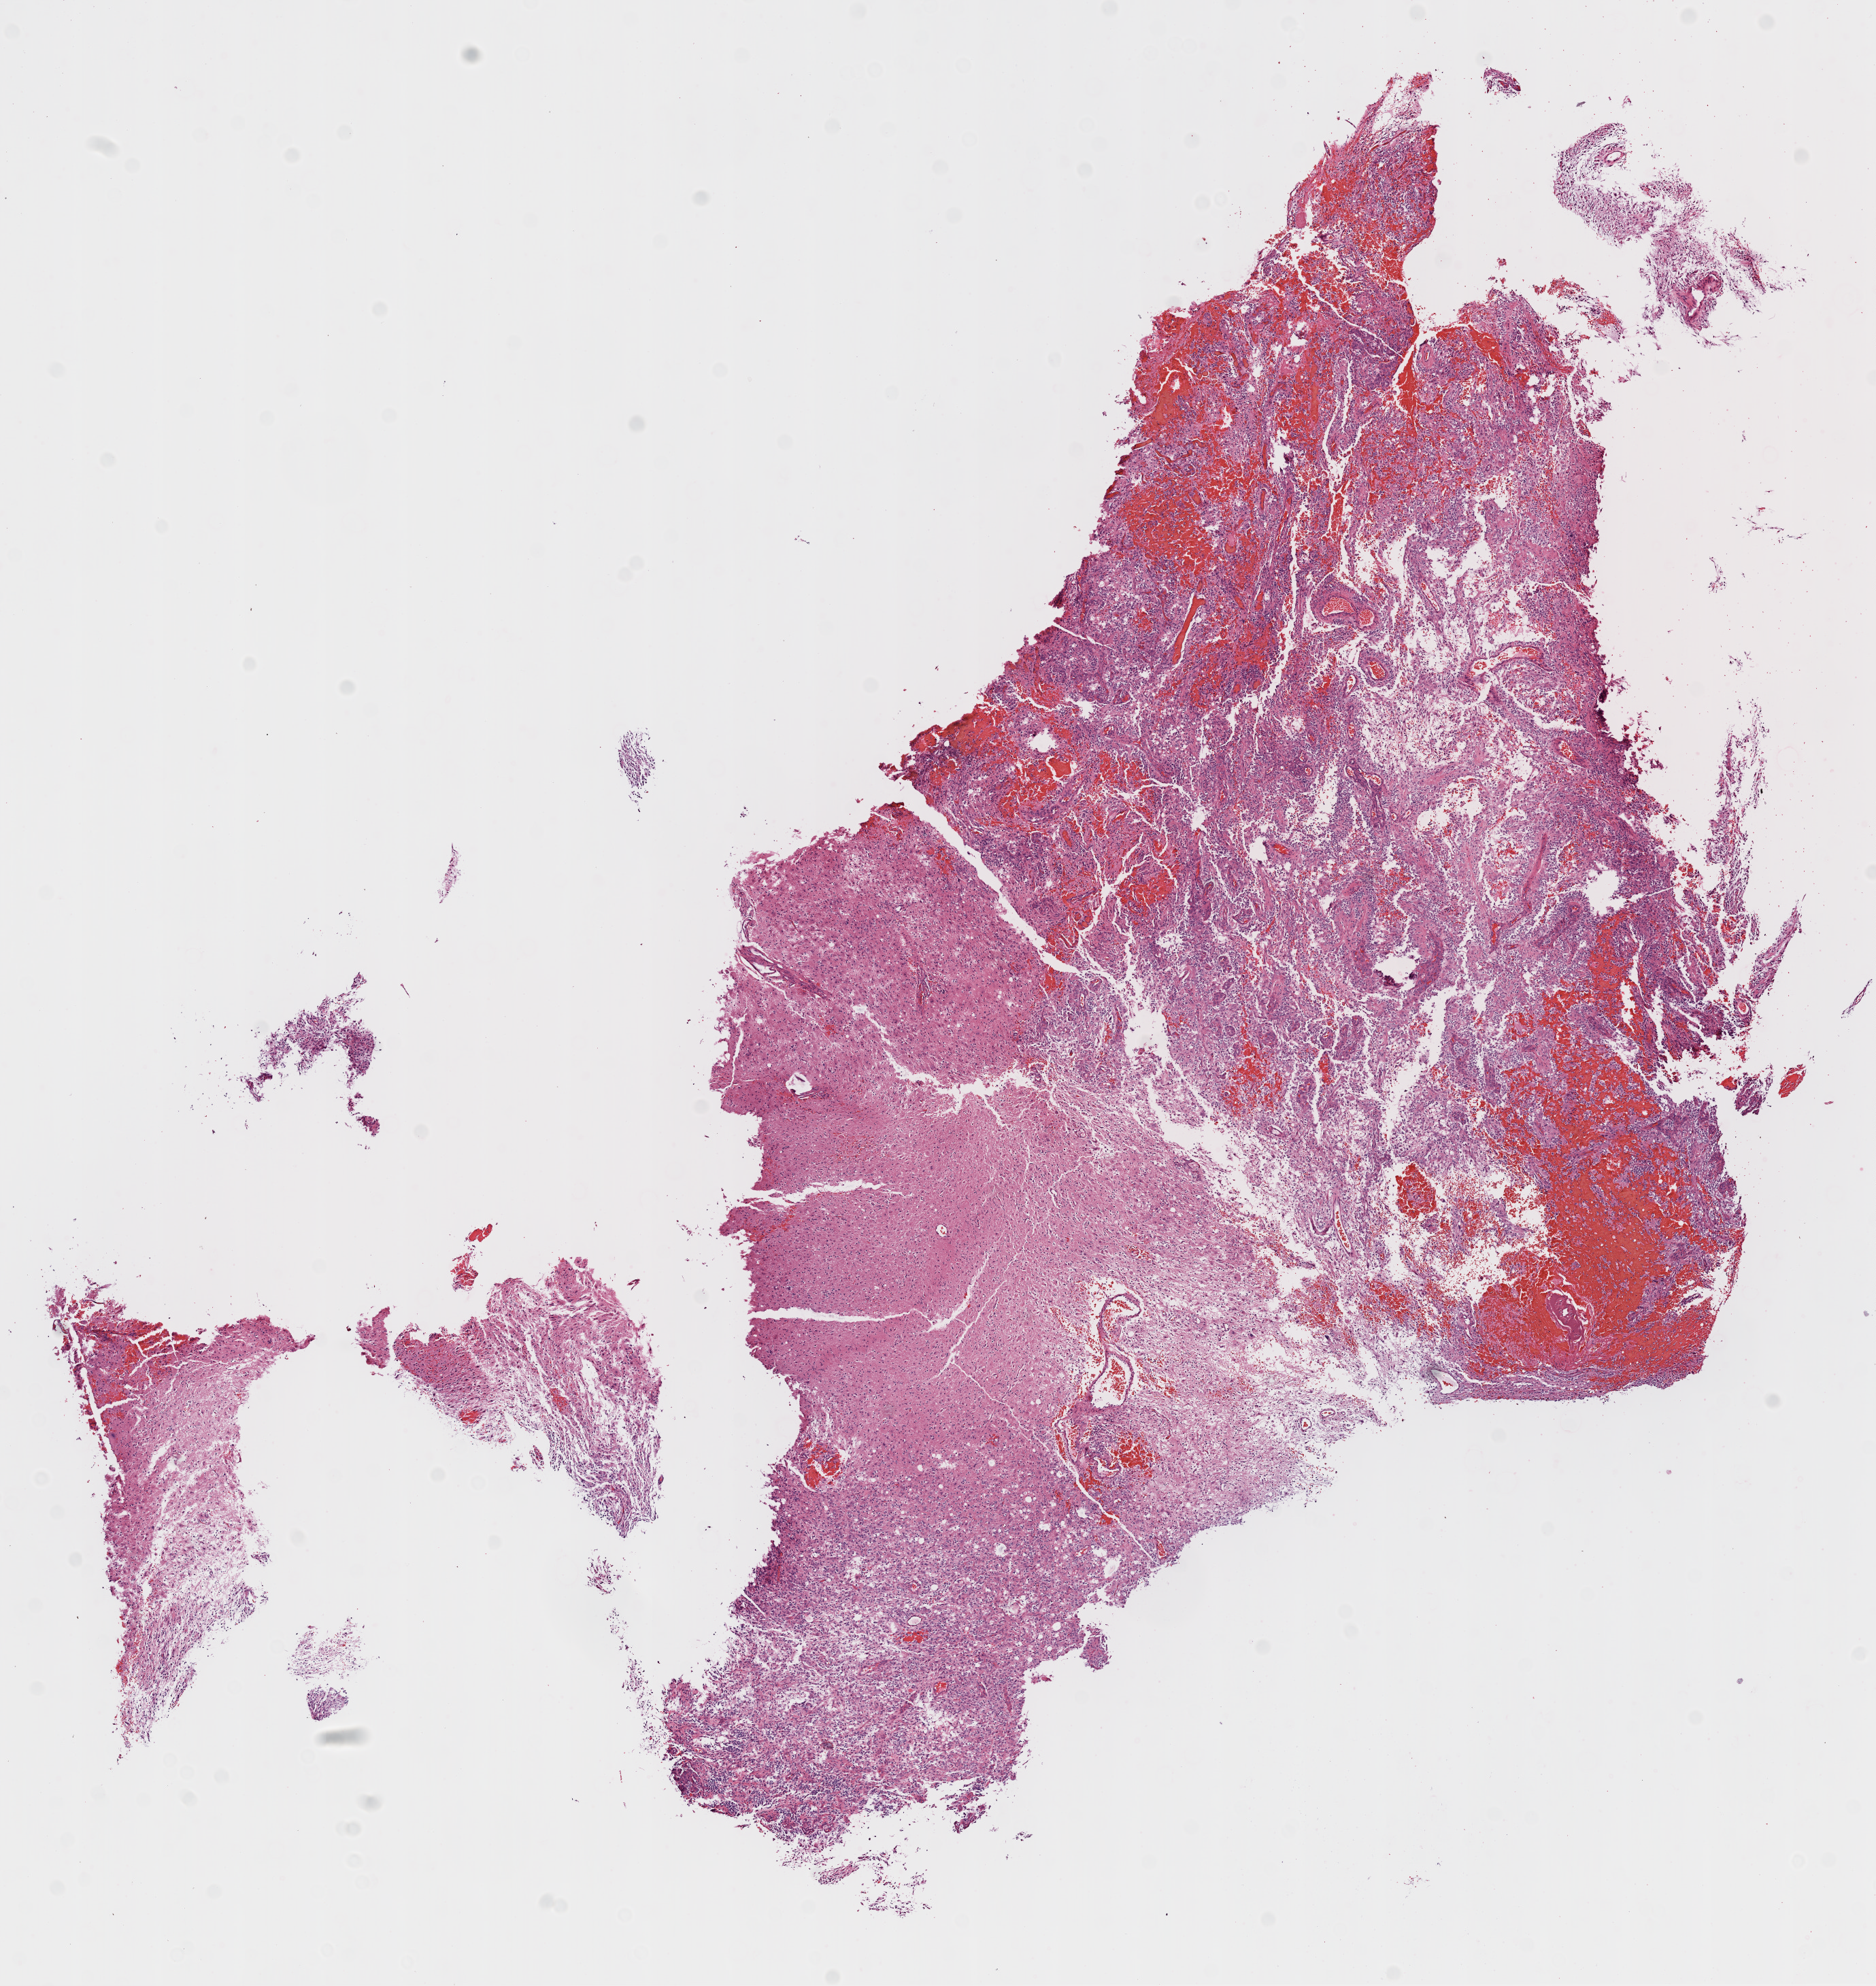
Hematoxylin and eosin (H&E) stained whole-slide image, shown as a low-resolution overview of the whole scanned area (about 11.1 x 11.8 mm, slide scanned at 20x). FFPE section. Primary tumour sample from the brain. Patient: male, age at initial diagnosis 51 years.
Diagnosis: Glioblastoma.